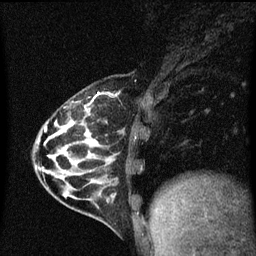
Breast MRI (dynamic contrast-enhanced), one sagittal slice. Slice 20 of 60 in the series (ordered by position). Dynamic contrast-enhanced series, image 2 of 3 at this slice position (ordered by acquisition). 1.5 T. TE 4.2 ms, TR 8.4 ms. 256 × 256 image matrix. Patient: female, 32 years.
Annotated regions visible in this slice (semi-automatically segmented with operator editing):
- analysis volume of interest (the breast-tissue region the enhancement analysis was run in; not a lesion): bounding box [x1, y1, x2, y2] px = [34, 86, 150, 169]
- tumour enhancement mask (voxels above the 70 % enhancement threshold inside the analysis volume of interest): [45, 92, 100, 131]